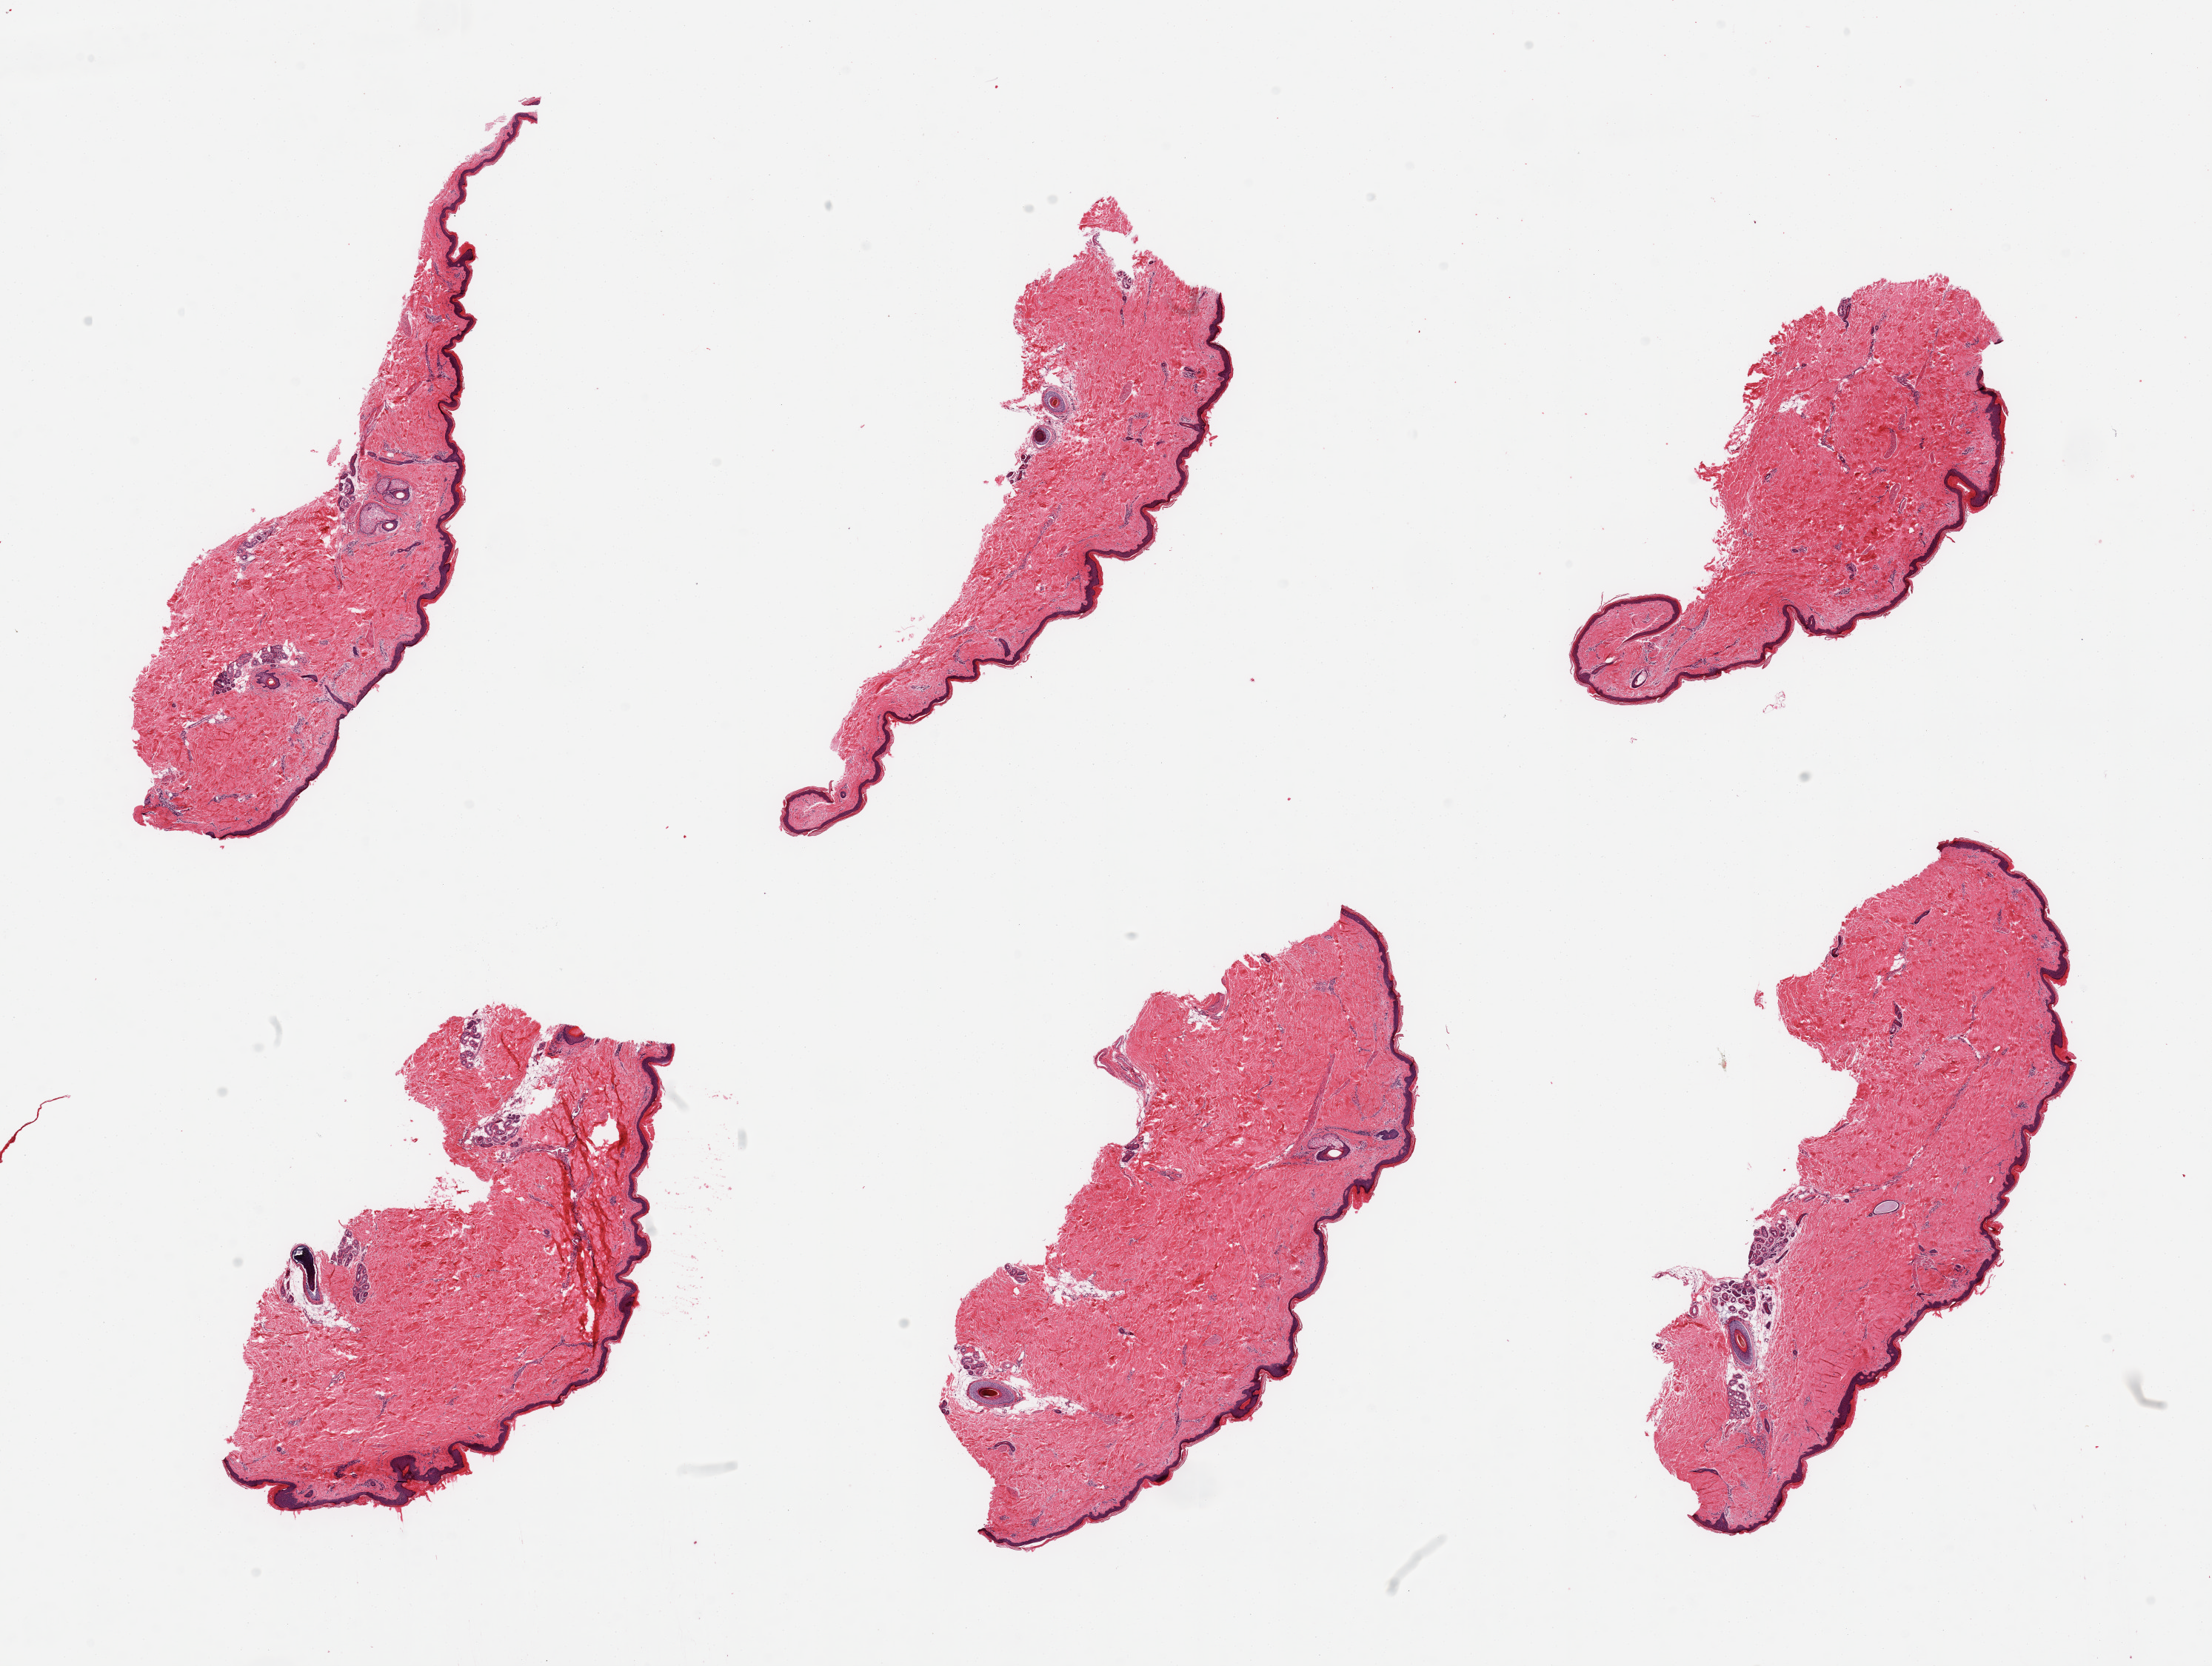
H&E whole-slide image, brightfield — shown as a low-resolution overview of the whole scanned area (about 23.6 x 17.8 mm). PAXgene-fixed, paraffin-embedded tissue. Section of skin of lower leg (target tissue). Tissue donor sample. Male donor.
Pathologist's review note for this sample: 6 pieces; well trimmed, small portion periadnexal fat.